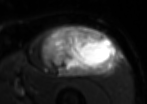
MRI of an extremity soft-tissue mass, one axial slice; slice 55 of 85 in the series (ordered by position); T2-weighted fat-saturated; MR volume resampled by the dataset authors to the PET/CT grid (not the native acquisition matrix); 3.27 mm slice thickness; 147 × 104 image matrix, field of view 144 × 102 mm. Male patient. From the clinical record (not read from this slice): histological type: extraskeletal osteosarcoma; grade: high; site of the primary tumour: thigh.
Annotated regions visible in this slice (expert contour drawn on MRI and transferred to this co-registered scan by the dataset authors):
- gross tumour volume (mass): bounding box [x1, y1, x2, y2] px = [40, 24, 121, 77]